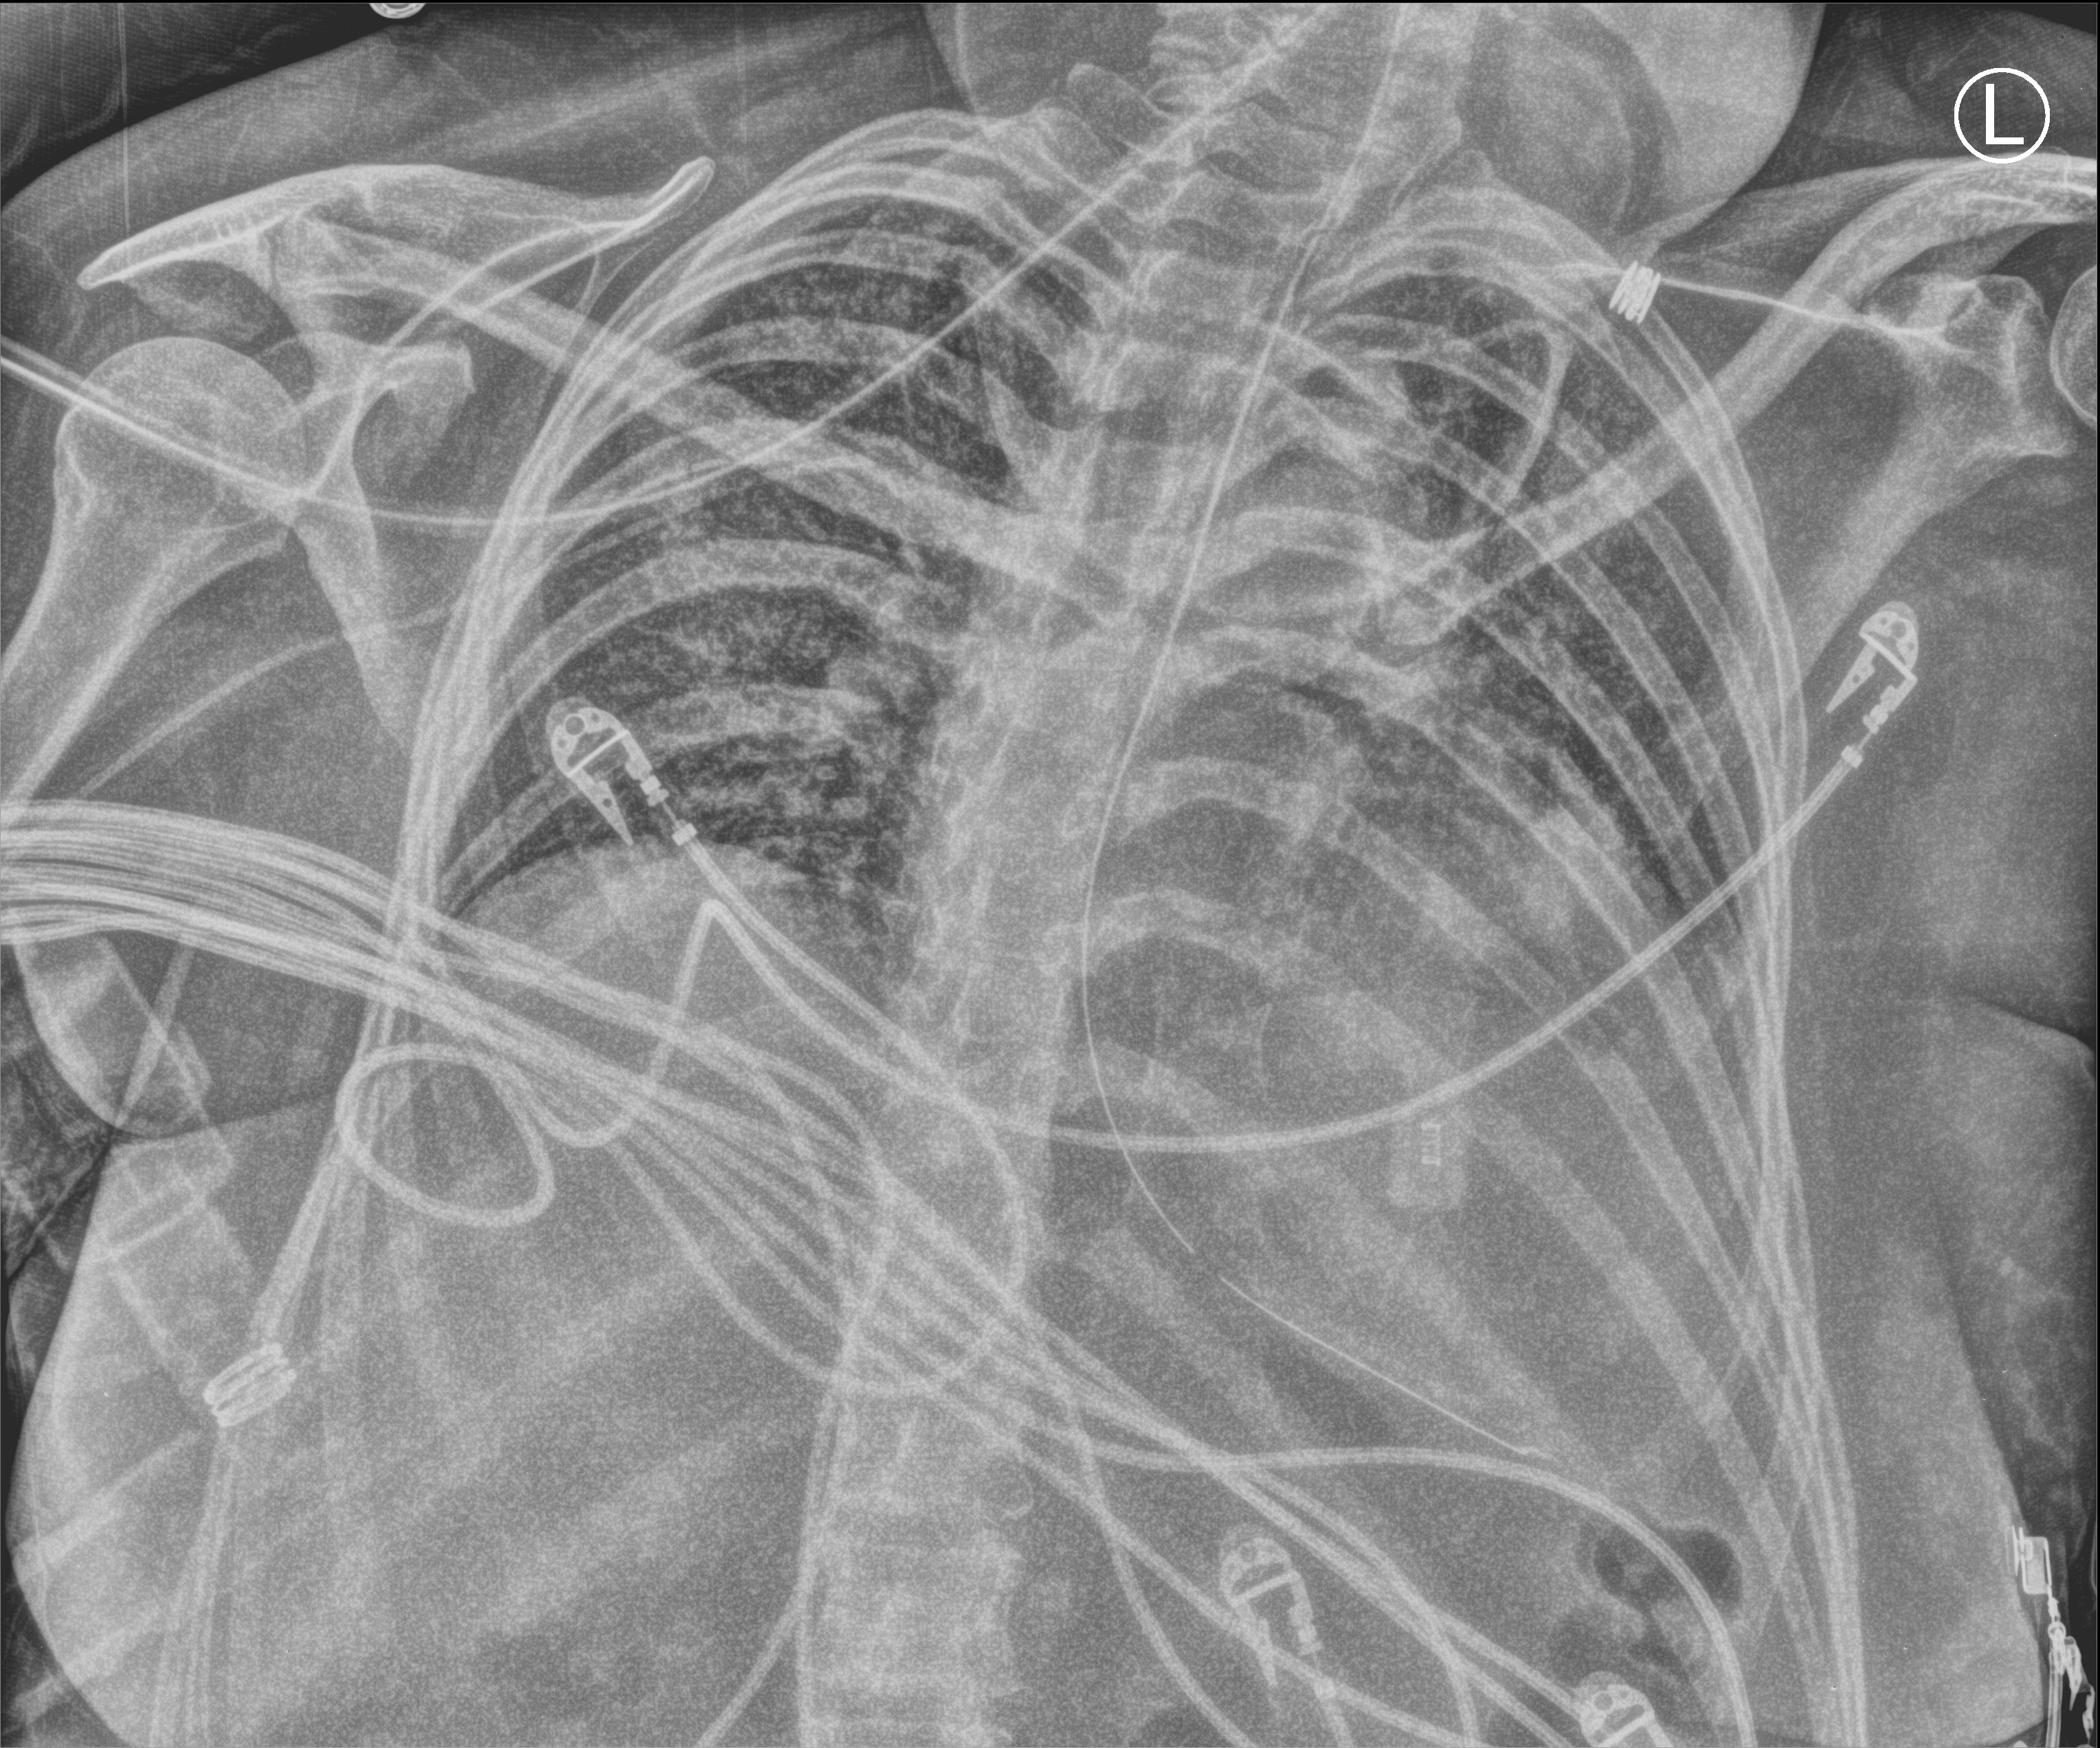
Portable chest radiograph; anteroposterior (AP) projection. Female patient hospitalised with COVID-19, age 18–59 years.
Hospital-stay facts (about this admission, not read from this image; timing relative to this image not recorded): mechanically ventilated during this hospital stay: yes; chronic kidney disease (admission record): no.